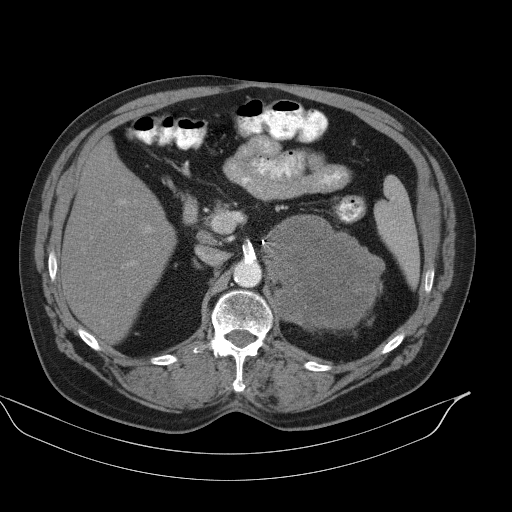
Contrast-enhanced abdominal CT, one axial slice; slice 64 of 92 in the series (ordered by position); reconstruction kernel B41s; 130 kVp; intravenous contrast given; soft-tissue window (W 400 / L 40 HU); 512 × 512 image matrix. Patient: male, 56 years. Case-level facts recorded for this patient, not image findings: diagnosis: adrenocortical carcinoma; tumour side: left adrenal; tumour size at pathology: 15 cm; Ki-67 index: 35 %; stage (as recorded): 4.
Annotated regions visible in this slice (semi-automatic segmentation, software-assisted and operator-edited):
- mass: box from (x=266, y=215) to (x=384, y=327) px